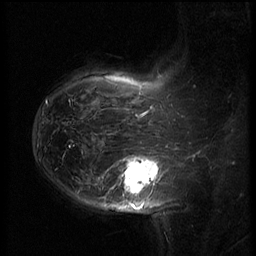
Breast MRI (dynamic contrast-enhanced), one sagittal slice; 3 images stored at this slice position (order not interpretable as contrast timing); 1.5 T; TE 4.2 ms, TR 8.9 ms; 2.5 mm slice thickness; 256 × 256 image matrix. Female patient, age 37 years. From the clinical record (not read from this slice): setting: breast cancer imaged before/during neoadjuvant chemotherapy; receptor status: triple-negative.
Structures marked on this image (semi-automatic segmentation, software-assisted and operator-edited):
- analysis volume of interest (the breast-tissue region the enhancement analysis was run in; not a lesion): bounding box [x1, y1, x2, y2] px = [116, 146, 168, 203]
- tumour enhancement mask (voxels above the 140 % enhancement threshold inside the analysis volume of interest): [121, 157, 159, 193]